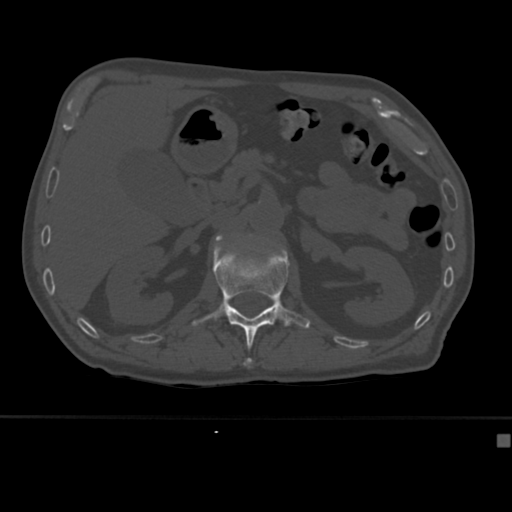
CT including the spine, one axial slice. Position 168 of 430 along the scan axis. Reconstruction kernel Br40s. Bone window (W 1800 / L 400 HU). 512 × 512 image matrix. Patient: male, 64 years. From the clinical record (not read from this slice): primary cancer: uterus.
Outlined on this slice (semi-automatically segmented with operator editing):
- L1 vertebra: bounding box [x1, y1, x2, y2] px = [192, 237, 310, 367]
- L2 vertebra: [216, 234, 223, 239]